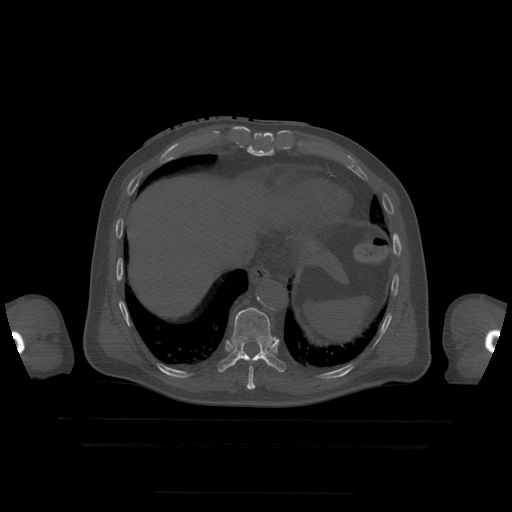
CT including the spine, one axial slice. Slice 246 of 522 in the series (ordered by position). Bone window (W 1800 / L 400 HU). 1.25 mm slice thickness. 512 × 512 image matrix, field of view 436 × 436 mm. Patient age 68 years. Case-level facts recorded for this patient, not image findings: primary cancer: urothelial.
Annotated regions visible in this slice (semi-automatic segmentation, software-assisted and operator-edited):
- T10 vertebra: bounding box (x1, y1, x2, y2) in pixels: (218, 308, 287, 373)
- T9 vertebra: (247, 367, 256, 390)